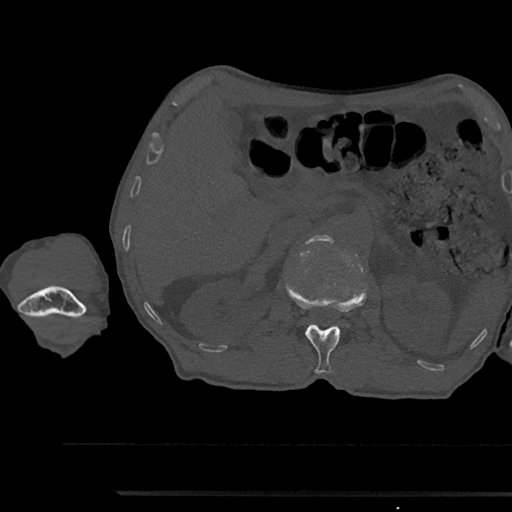
CT including the spine, one axial slice. Position 620 of 797 along the scan axis. Reconstruction kernel Br40s/3. 120 kVp. Bone window (W 1800 / L 400 HU). 0.5 mm slice thickness. 512 × 512 image matrix. Male patient, age 79 years. Case-level facts recorded for this patient, not image findings: primary cancer: prostate.
Outlined on this slice (semi-automatic segmentation, software-assisted and operator-edited):
- L1 vertebra: bounding box (x1, y1, x2, y2) in pixels: (287, 284, 366, 374)
- L2 vertebra: (307, 235, 334, 244)